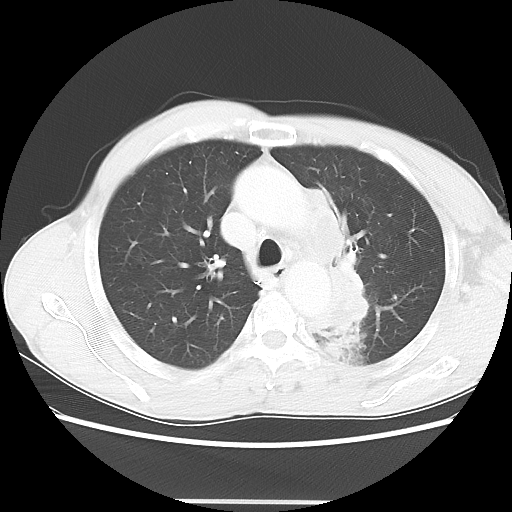
Chest CT, one axial slice. Position 46 of 62 along the scan axis. Reconstruction kernel LUNG. 100 kVp. Lung window (W 1500 / L -600 HU). 5 mm slice thickness. 512 × 512 image matrix, field of view 360 × 360 mm. Male patient, age 61 years. Case-level facts recorded for this patient, not image findings: clinical TNM (as recorded): T3 N1 M1.
Annotated regions visible in this slice (rectangle marked by the reading radiologist):
- lung tumour (recorded histology: adenocarcinoma): bounding box (x1, y1, x2, y2) in pixels: (299, 177, 378, 353)